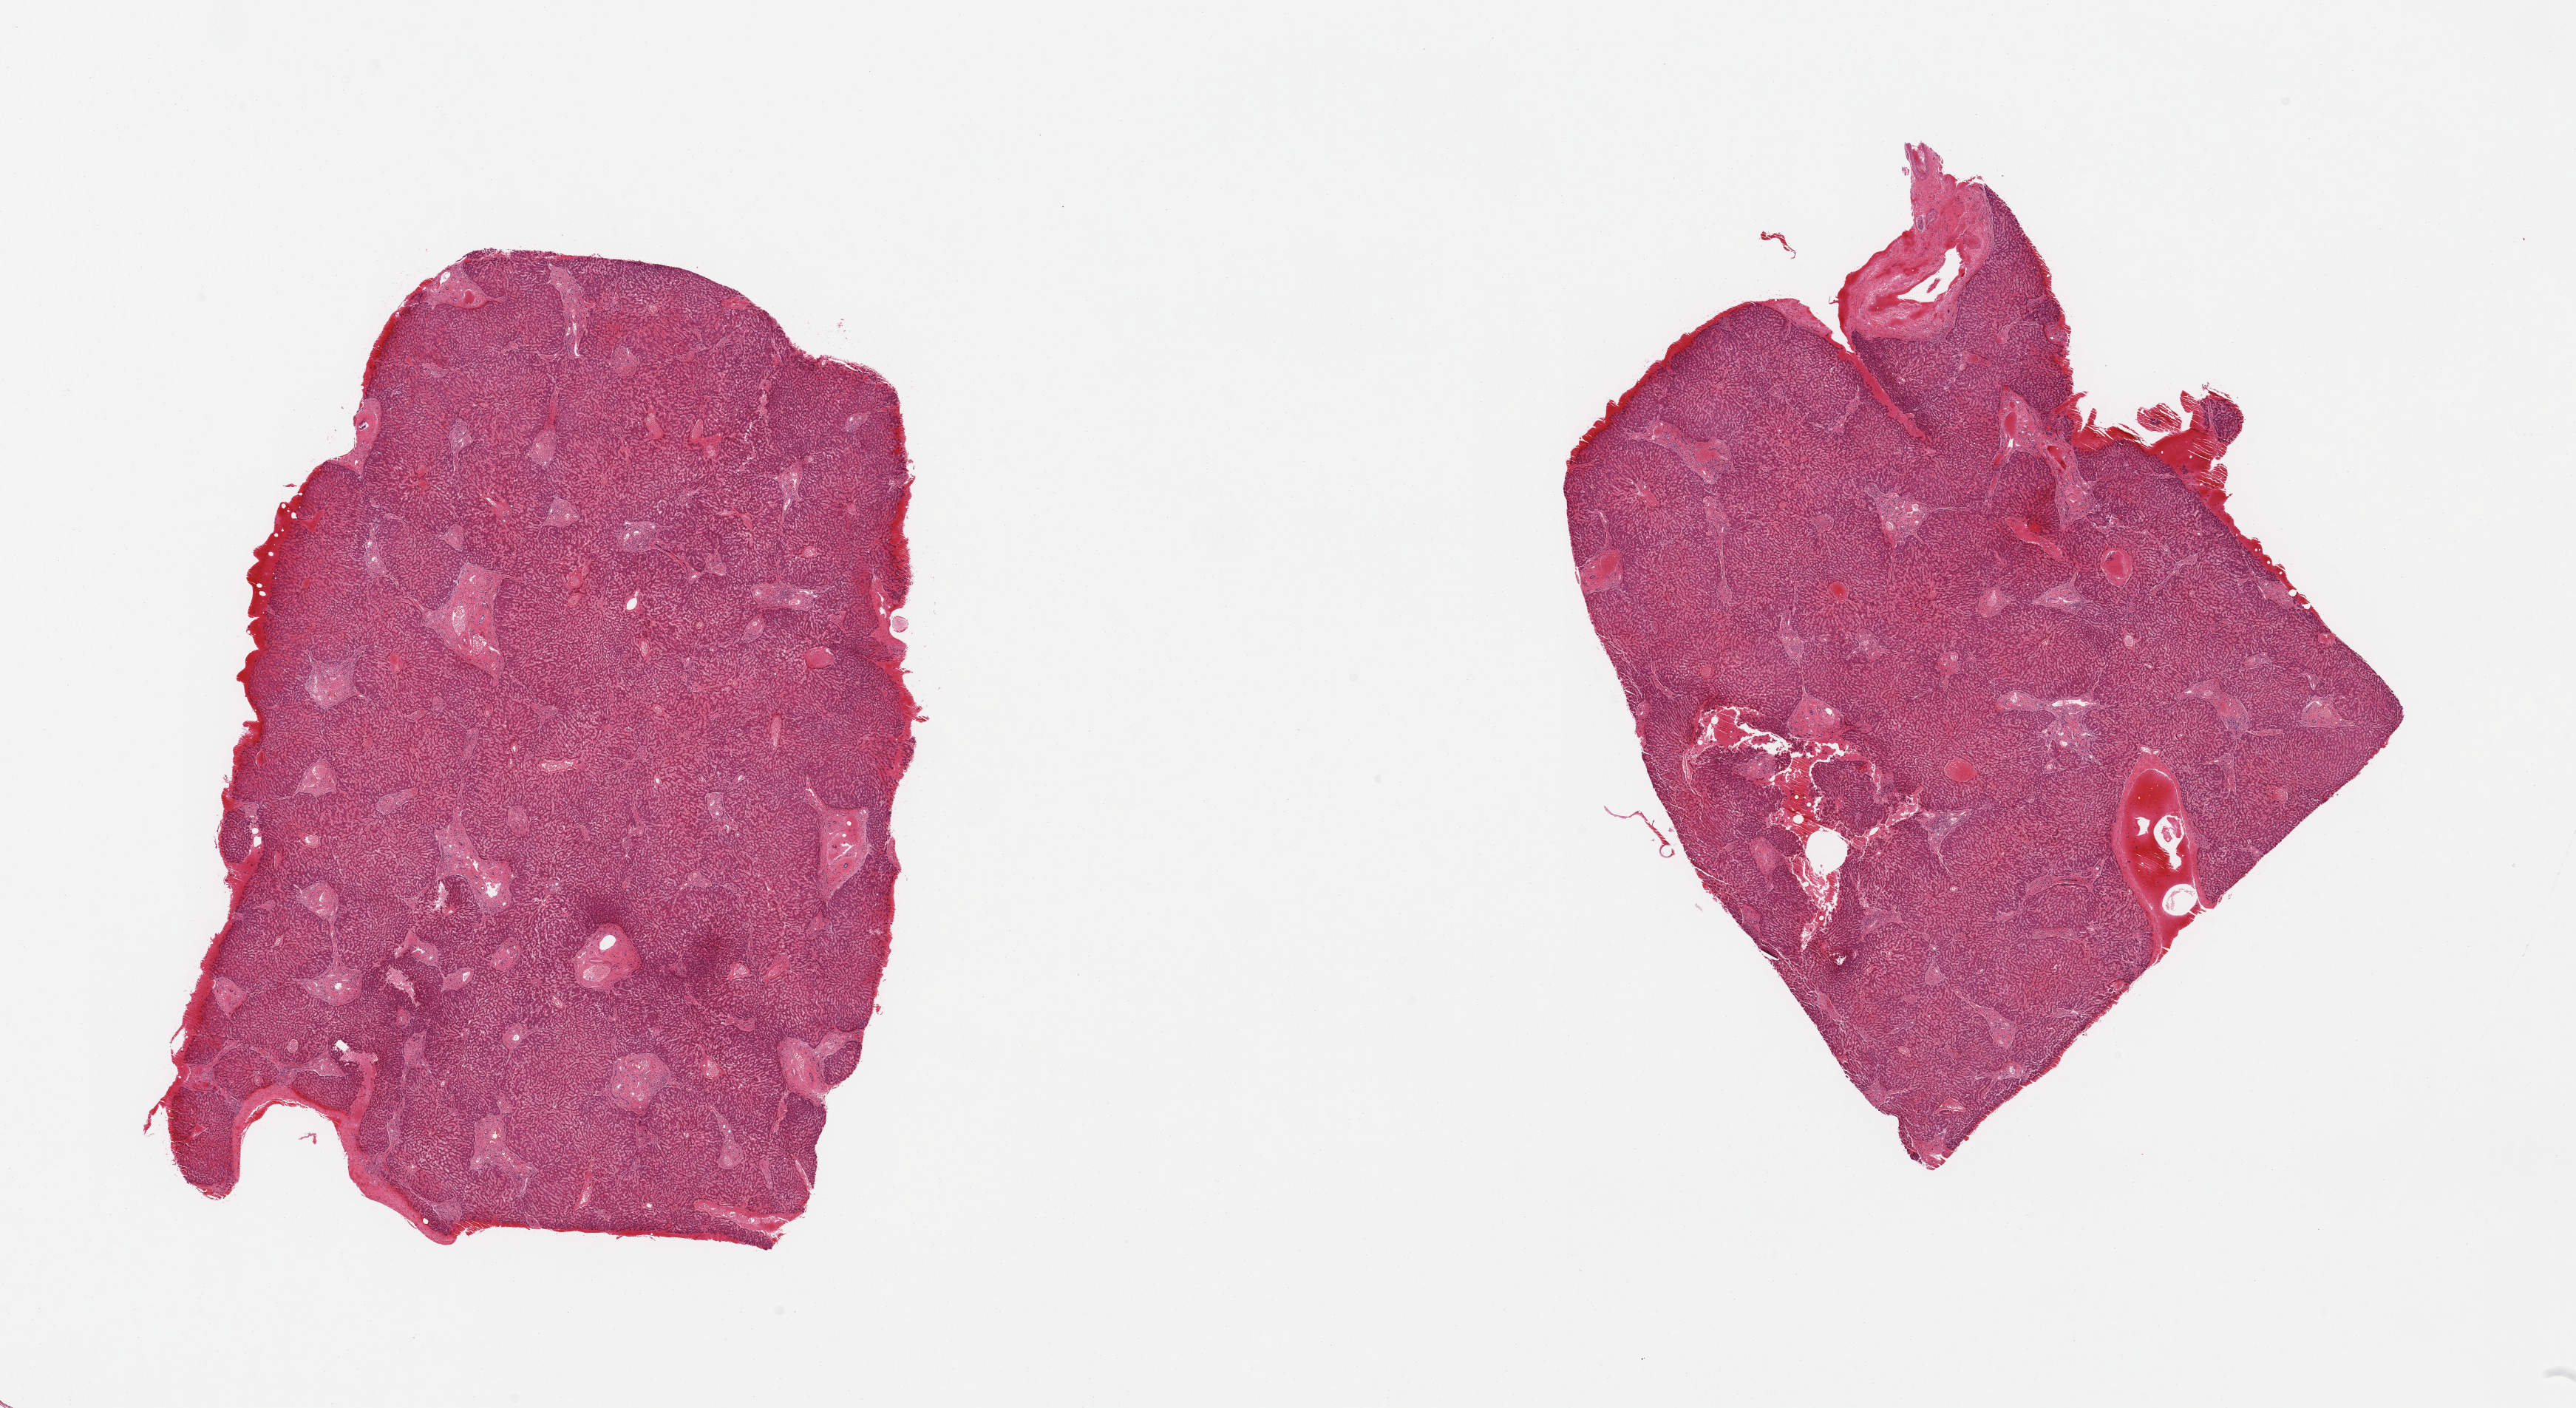
H&E whole-slide image, brightfield — whole scanned area (about 27.6 x 15.1 mm) shown as a low-resolution overview, PAXgene-fixed paraffin-embedded (PFPE) section, target tissue: liver, tissue donor sample. Male donor.
- reviewer comment on this tissue sample: 2 pieces; central congestion